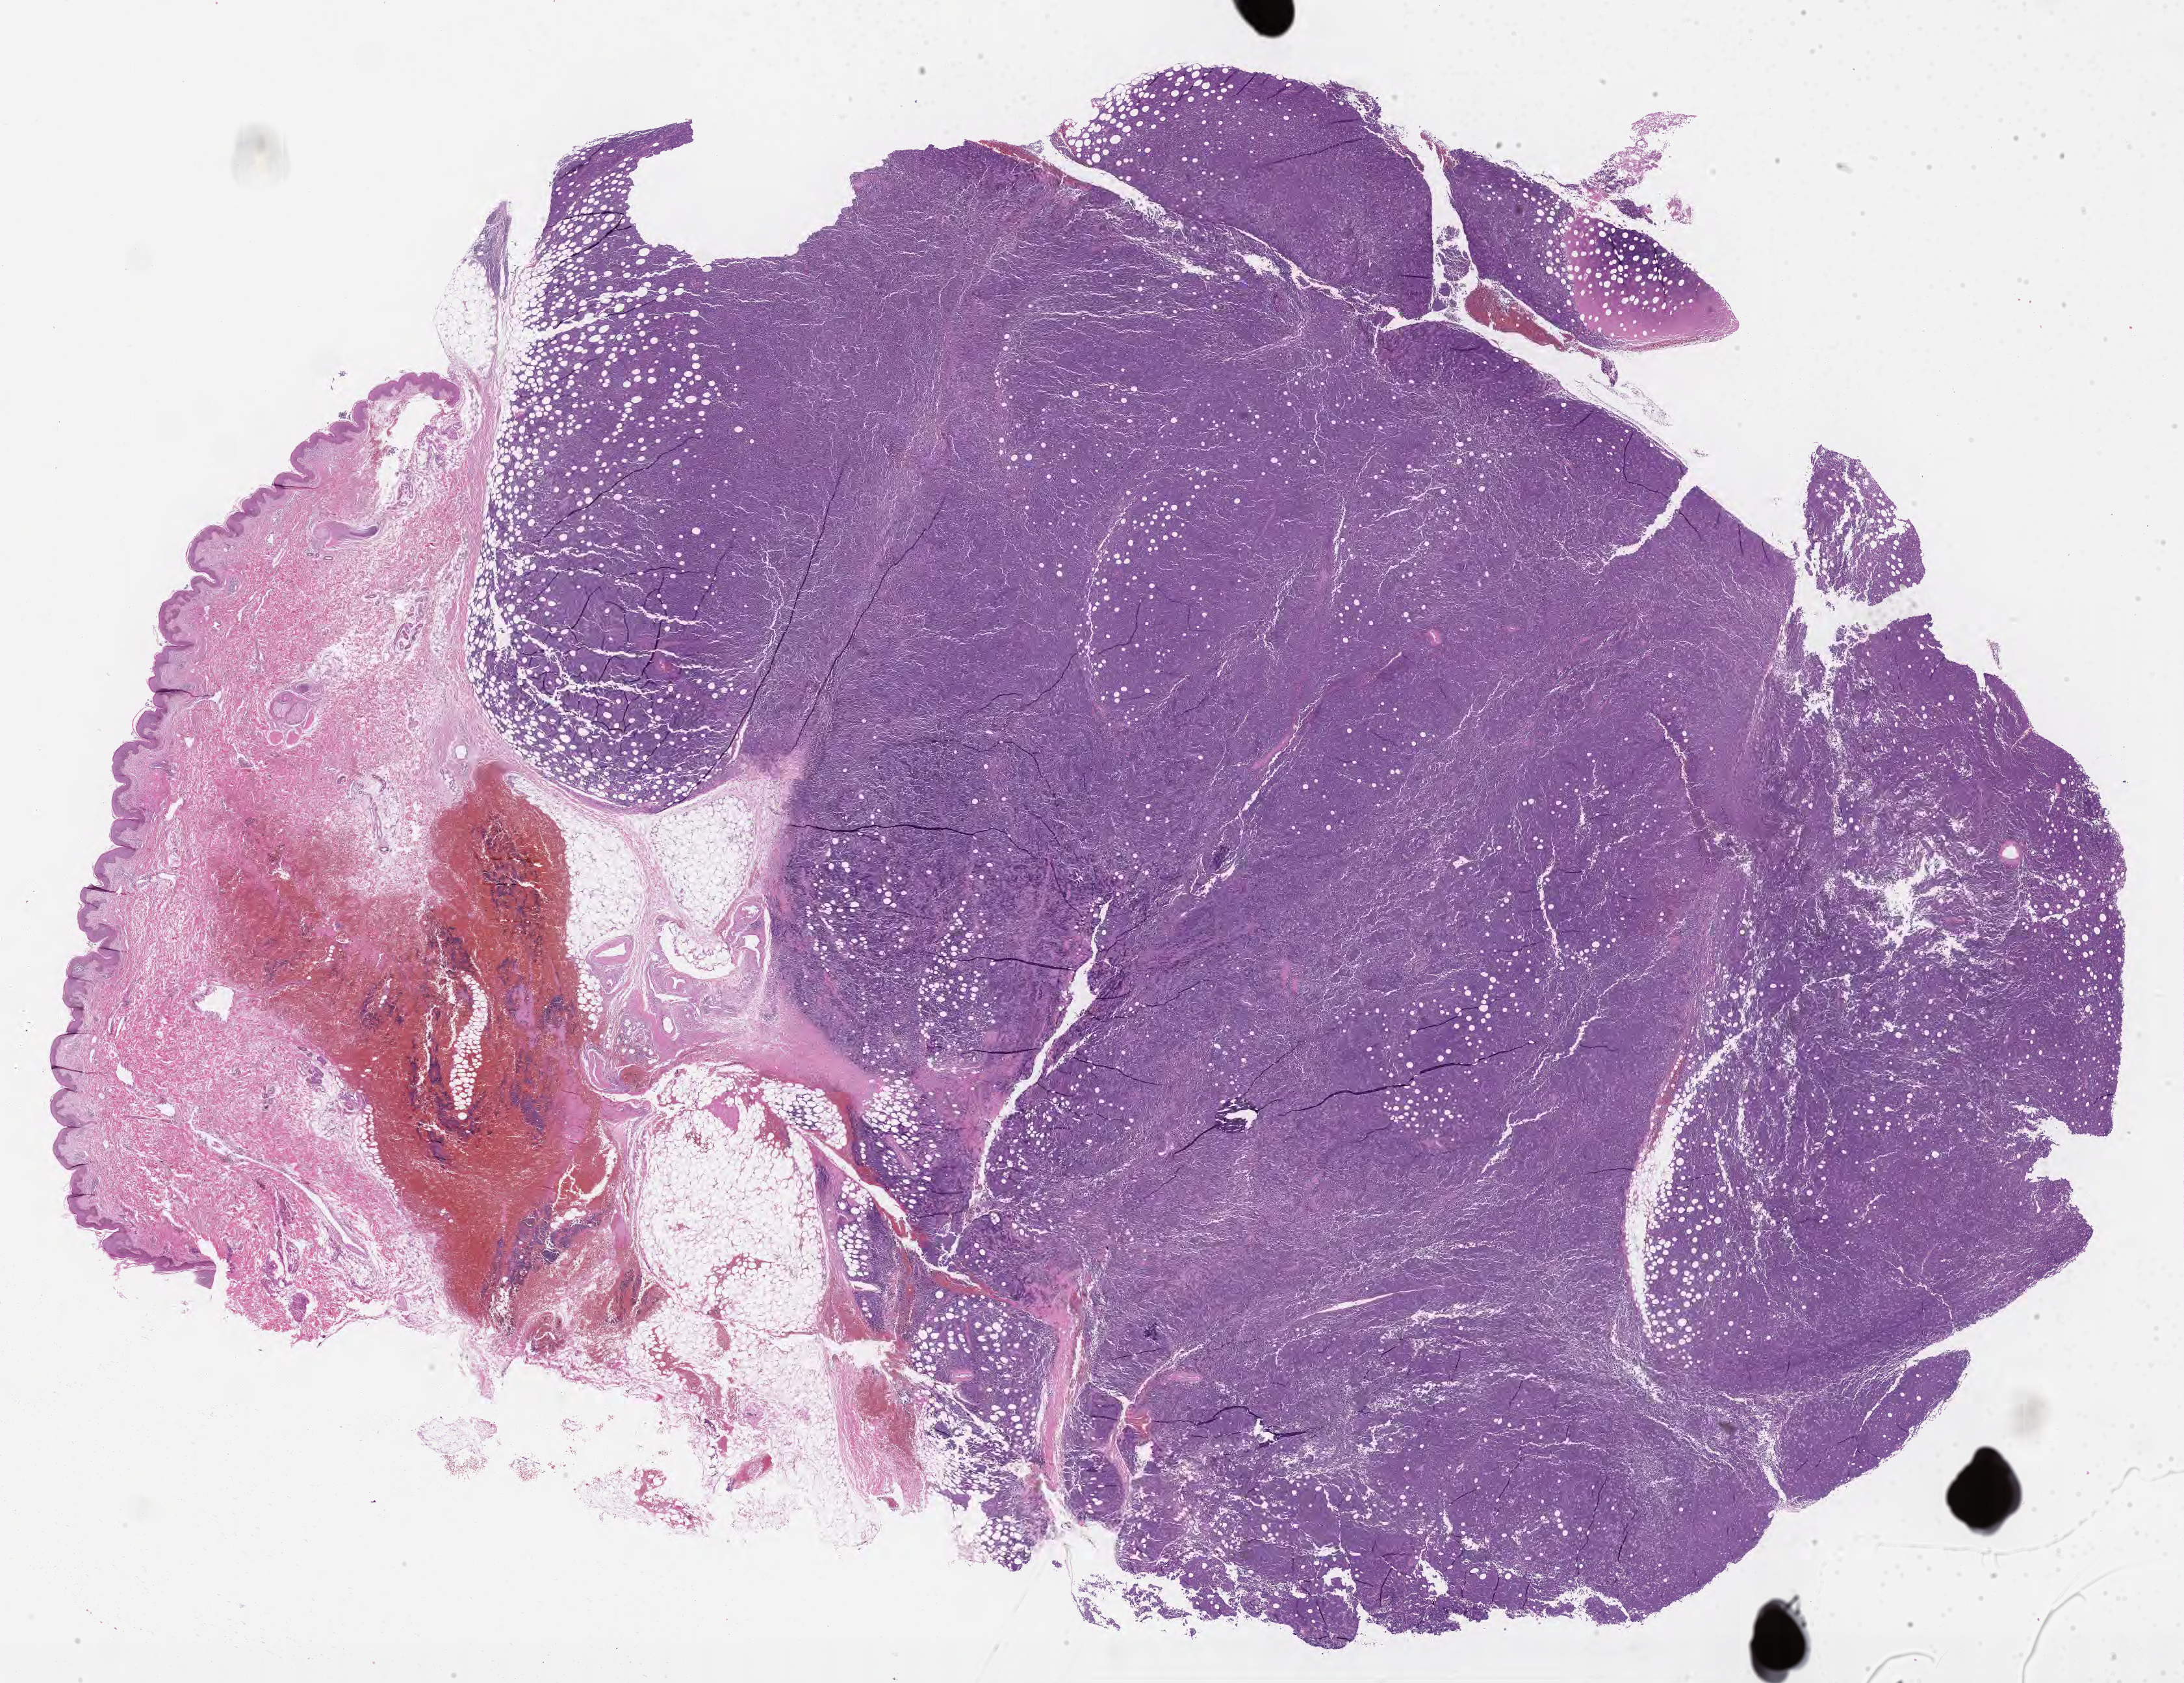
Whole-slide image, H&E stain — whole scanned area (about 27.2 x 20.9 mm) shown as a low-resolution overview. Tumor tissue. Male patient, aged 52.
Histologic diagnosis: Burkitt lymphoma, NOS.